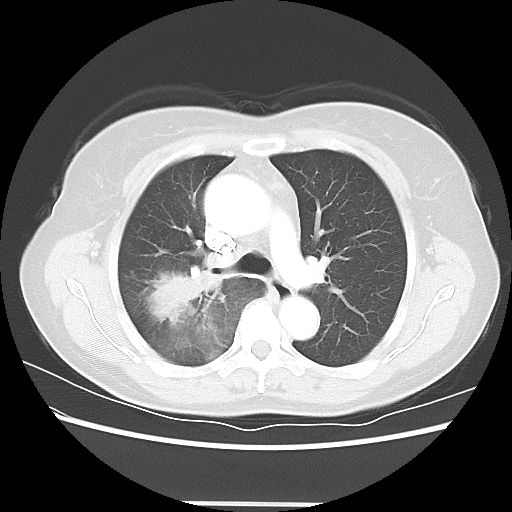
Chest CT, one axial slice; position 39 of 56 along the scan axis; reconstruction kernel LUNG; 120 kVp; lung window (W 1500 / L -600 HU); 5 mm slice thickness; 512 × 512 image matrix, field of view 360 × 360 mm. Female patient, age 55 years. From the clinical record (not read from this slice): clinical TNM (as recorded): T2 N1 M0; histopathological grade: G2-3.
Structures marked on this image (bounding box drawn by a radiologist):
- lung tumour (recorded histology: adenocarcinoma): bounding box (x1, y1, x2, y2) in pixels: (136, 263, 237, 341)